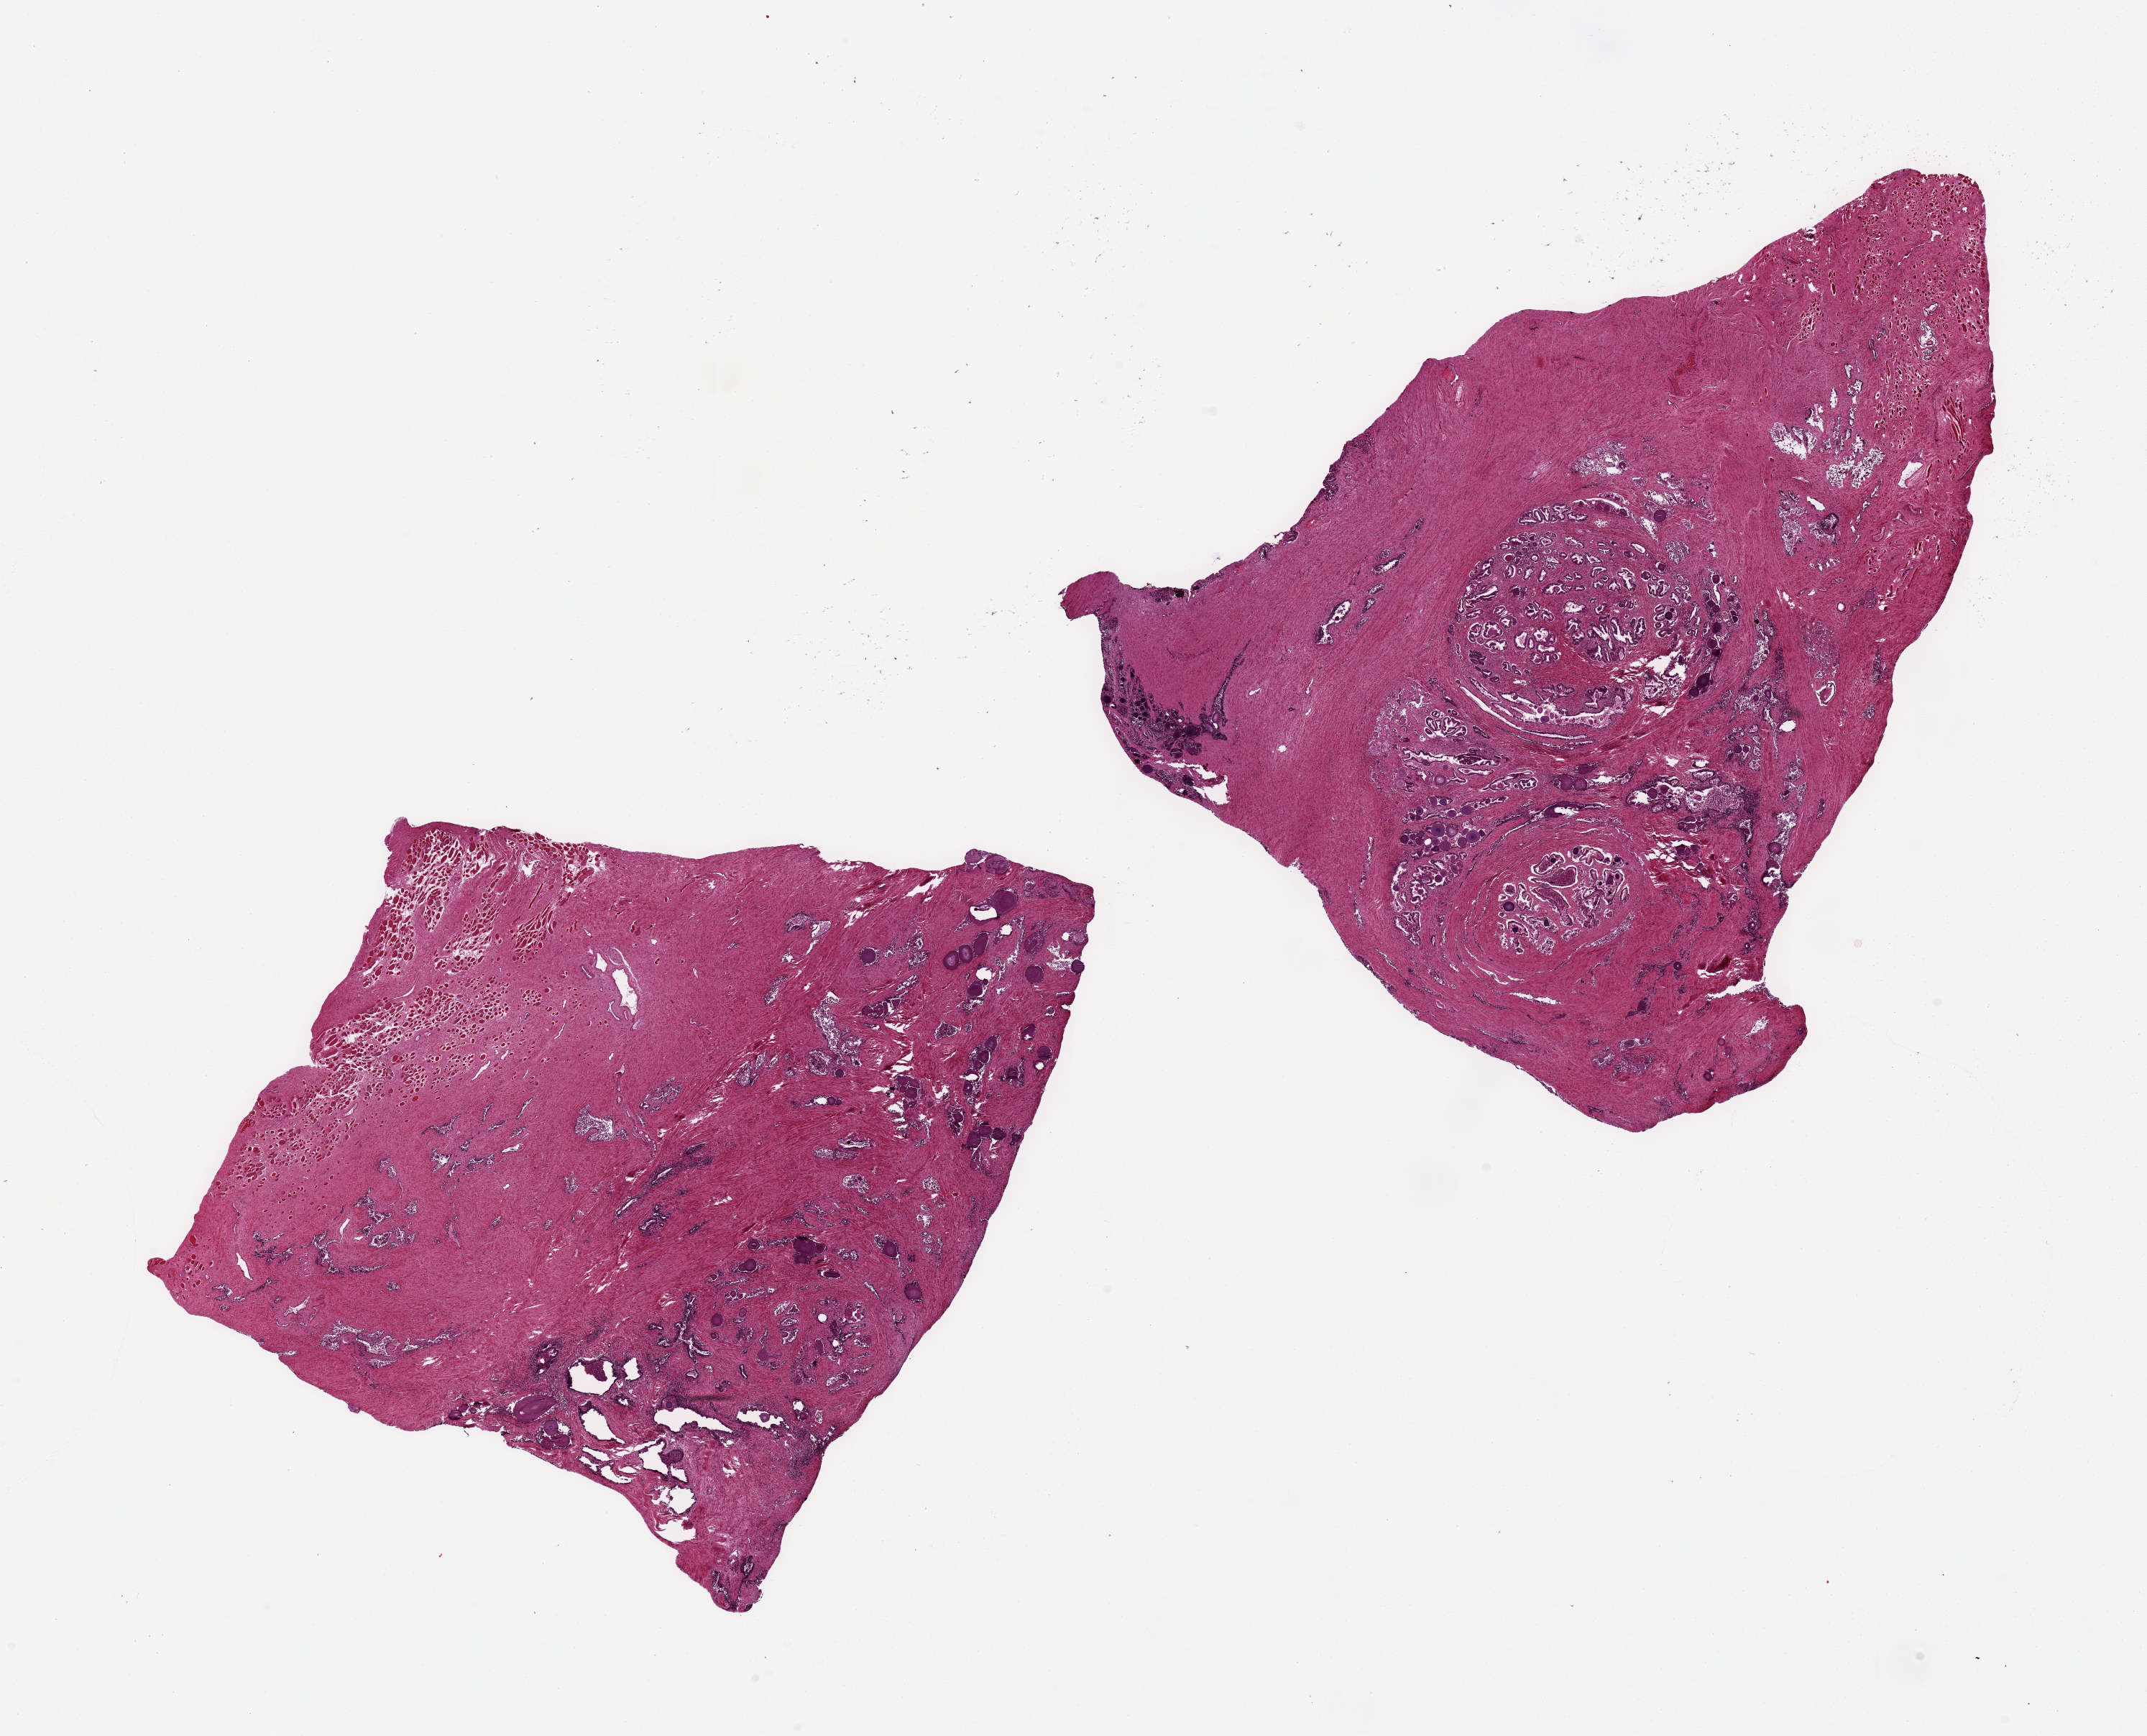
H&E whole-slide image — low-resolution overview of the scanned area, about 23.6 x 19.1 mm (acquisition: 20x scan), PAXgene-fixed, paraffin-embedded tissue, section of prostate (target tissue), donor tissue sample.
Pathologist's review note for this sample: 2 pieces, each ~9x8mm. Glandular and stromal hyperplasia, chronic prostatitis.